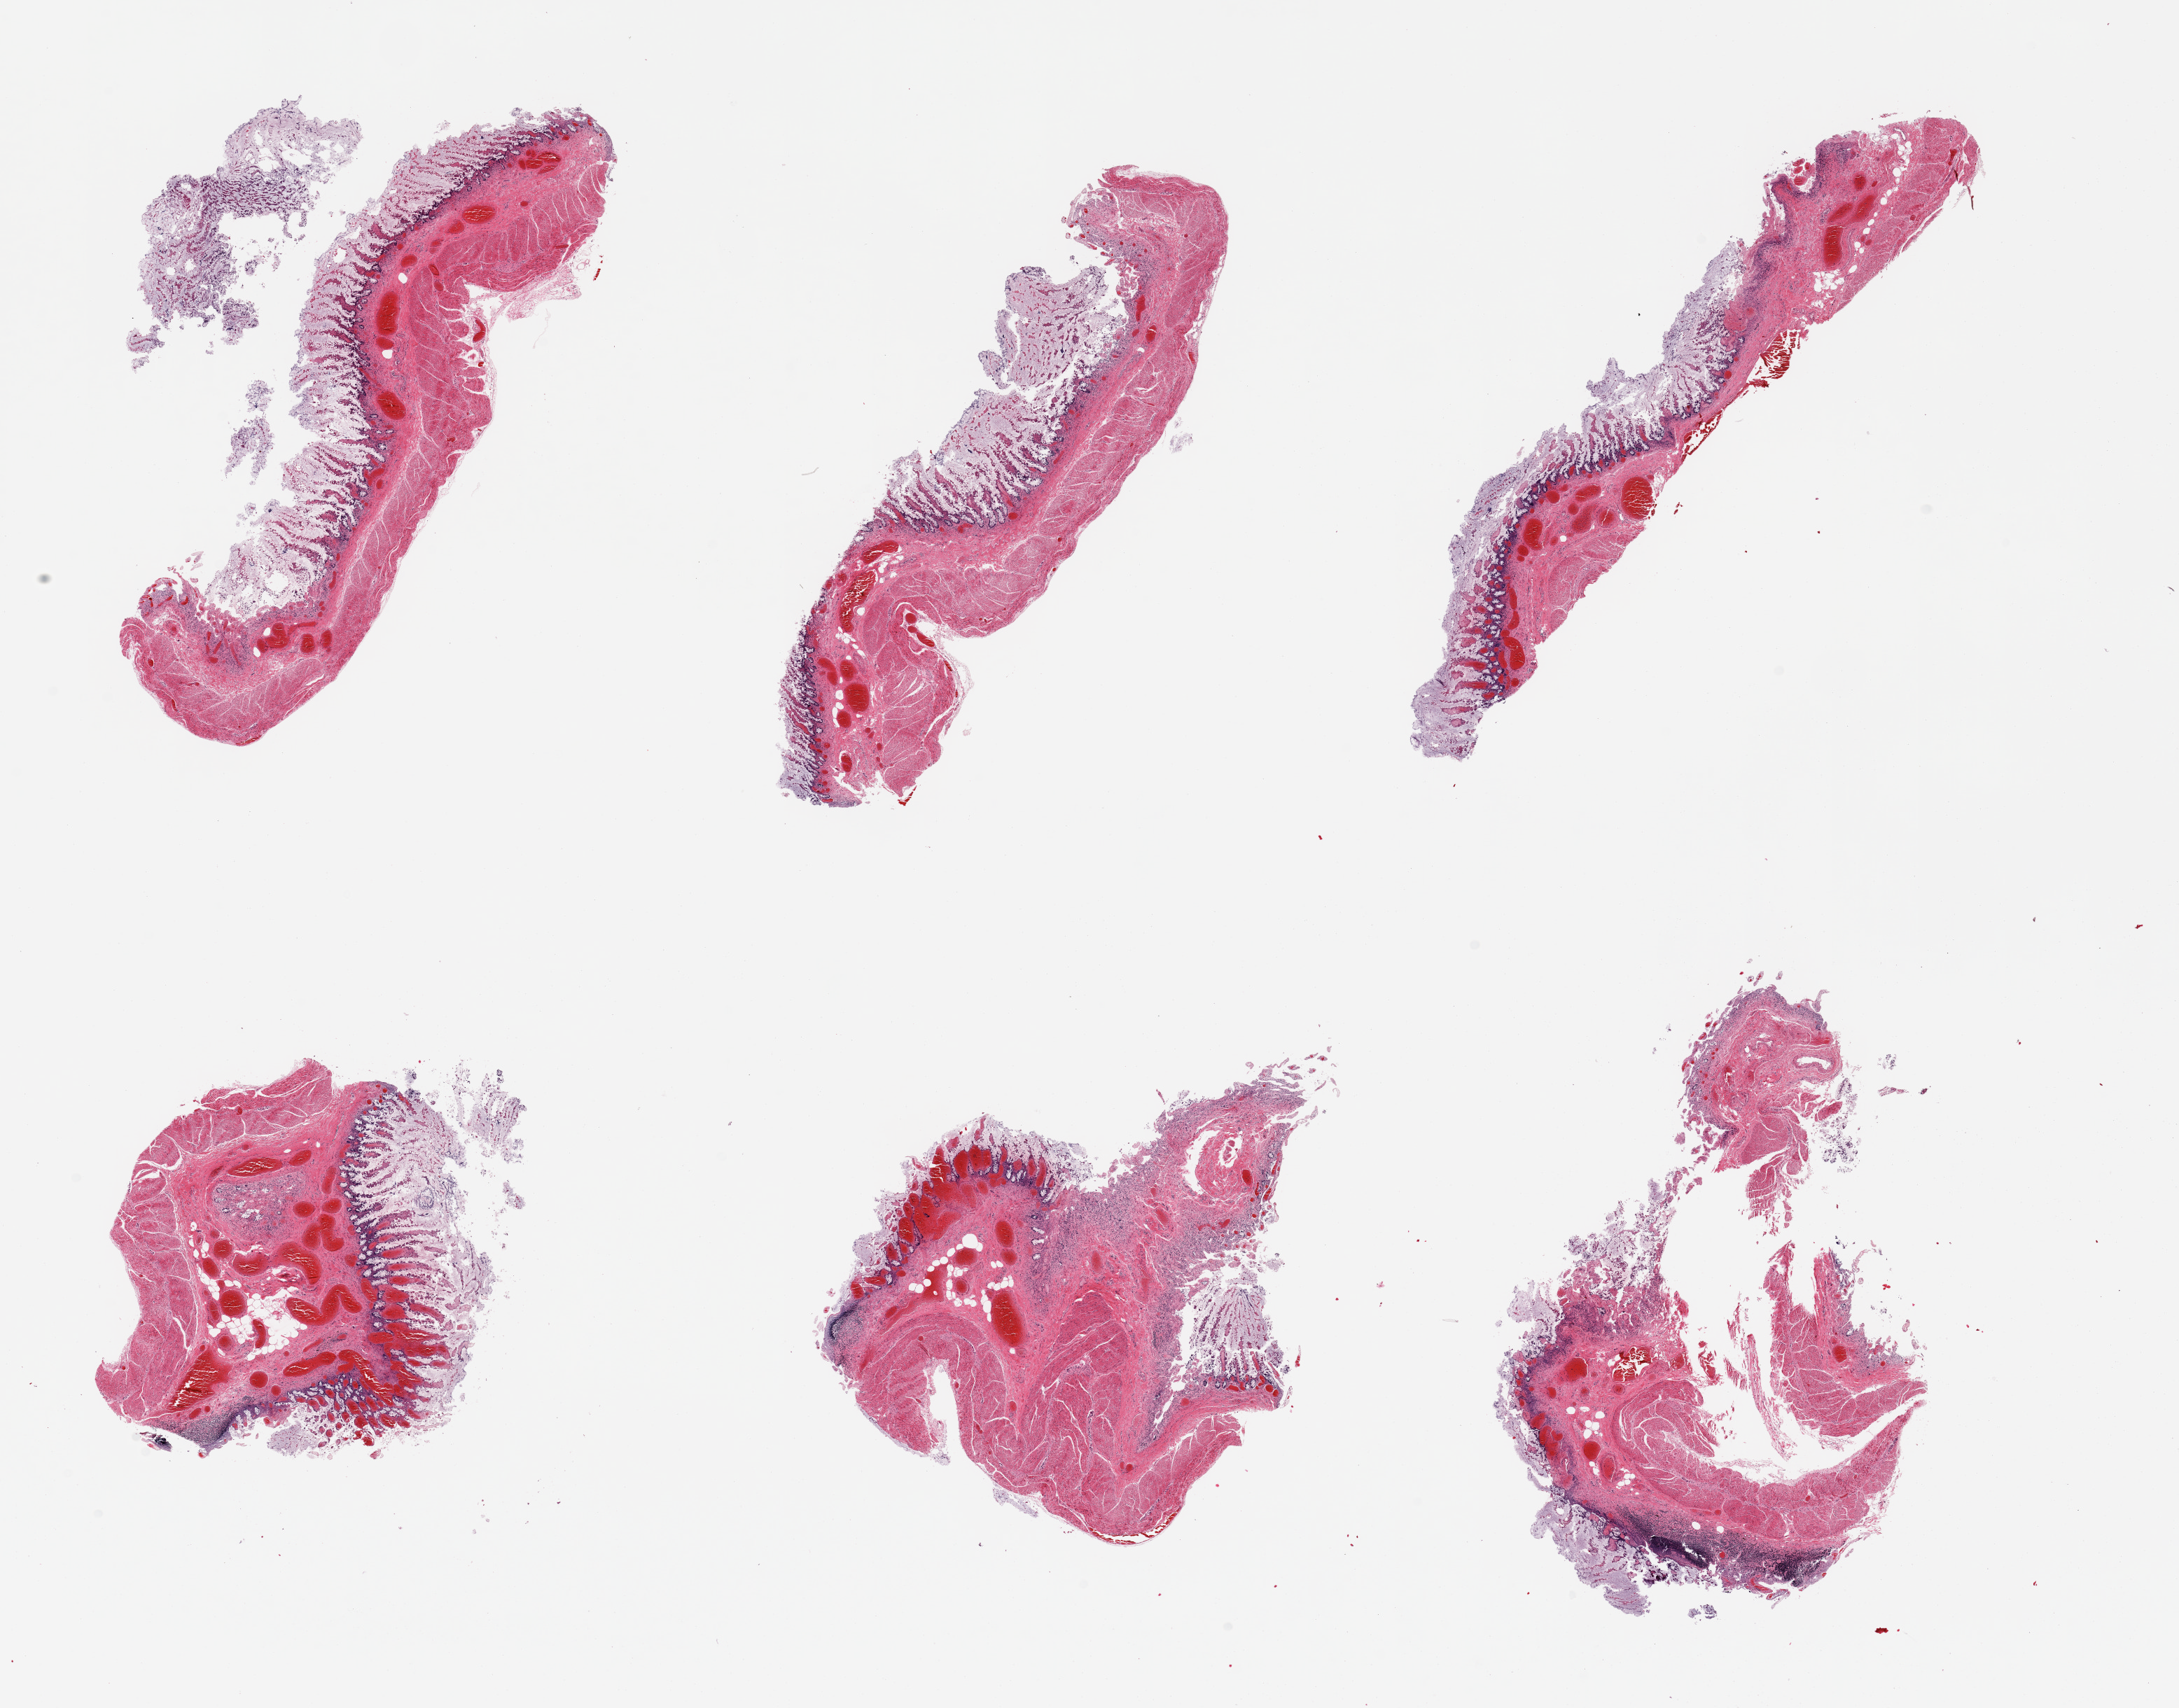
Whole-slide image, hematoxylin and eosin (H&E) stain, low-resolution overview of the scanned area, about 24.6 x 19.3 mm, PAXgene-fixed, paraffin-embedded tissue, sampled site (target tissue): ileum, tissue donor sample.
Review note (as recorded): 6 pieces; 2 deposits of autolyzed lymphoid tissue.